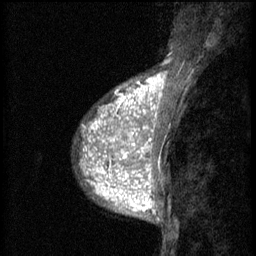
Breast MRI (dynamic contrast-enhanced), one sagittal slice. Slice 18 of 60 in the series (ordered by position). 3 images stored at this slice position (order not interpretable as contrast timing). 1.5 T. TE 4.2 ms, TR 8.2 ms. 256 × 256 image matrix, field of view 180 × 180 mm. Female patient, age 38 years.
Annotated regions visible in this slice (semi-automatic segmentation, software-assisted and operator-edited):
- analysis volume of interest (the breast-tissue region the enhancement analysis was run in; not a lesion): bounding box [x1, y1, x2, y2] px = [92, 112, 152, 171]
- tumour enhancement mask (voxels above the 70 % enhancement threshold inside the analysis volume of interest): [92, 112, 152, 171]